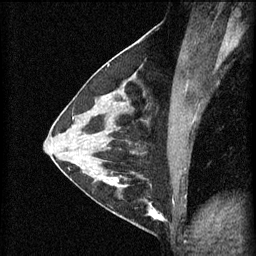
Breast MRI (dynamic contrast-enhanced), one sagittal slice. Position 30 of 60 along the scan axis. 3 images stored at this slice position (order not interpretable as contrast timing). 1.5 T. TE 4.2 ms, TR 11 ms. 256 × 256 image matrix, field of view 180 × 180 mm. Patient: female, 29 years.
Outlined on this slice (semi-automatic segmentation, software-assisted and operator-edited):
- analysis volume of interest (the breast-tissue region the enhancement analysis was run in; not a lesion): box from (x=105, y=172) to (x=168, y=227) px
- tumour enhancement mask (voxels above the 70 % enhancement threshold inside the analysis volume of interest): (x=108, y=172)–(x=168, y=221)